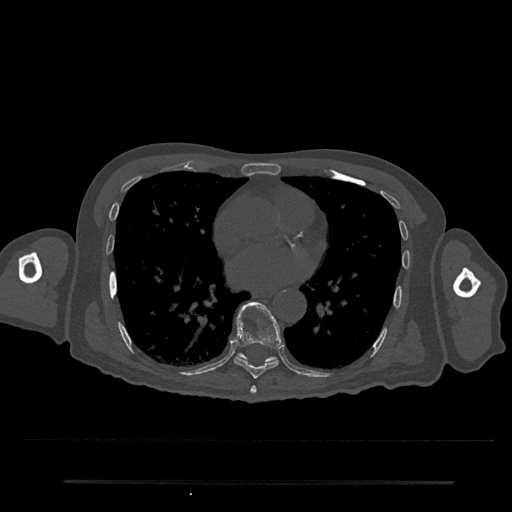
CT including the spine, one axial slice; position 410 of 797 along the scan axis; reconstruction kernel Br40s/3; bone window (W 1800 / L 400 HU); 512 × 512 image matrix, field of view 427 × 427 mm. Patient: male, 74 years. Case-level facts recorded for this patient, not image findings: primary cancer: prostate.
Annotated regions visible in this slice (semi-automatically segmented with operator editing):
- T7 vertebra: box from (x=250, y=386) to (x=257, y=394) px
- T8 vertebra: (x=234, y=302)–(x=282, y=379)
- T9 vertebra: (x=239, y=353)–(x=276, y=362)